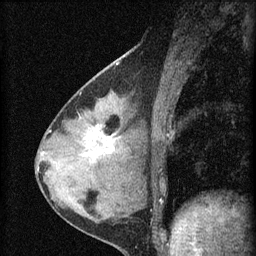
Breast MRI (dynamic contrast-enhanced), one sagittal slice; slice 26 of 60 in the series (ordered by position); dynamic contrast-enhanced series, image 2 of 4 at this slice position (ordered by acquisition); 1.5 T; TE 4.2 ms, TR 8.2 ms; 2 mm slice thickness; 256 × 256 image matrix, field of view 180 × 180 mm. Female patient, age 37 years.
Annotated regions visible in this slice (semi-automatic segmentation, software-assisted and operator-edited):
- analysis volume of interest (the breast-tissue region the enhancement analysis was run in; not a lesion): bounding box [x1, y1, x2, y2] px = [77, 116, 127, 175]
- tumour enhancement mask (voxels above the 70 % enhancement threshold inside the analysis volume of interest): [91, 124, 115, 157]